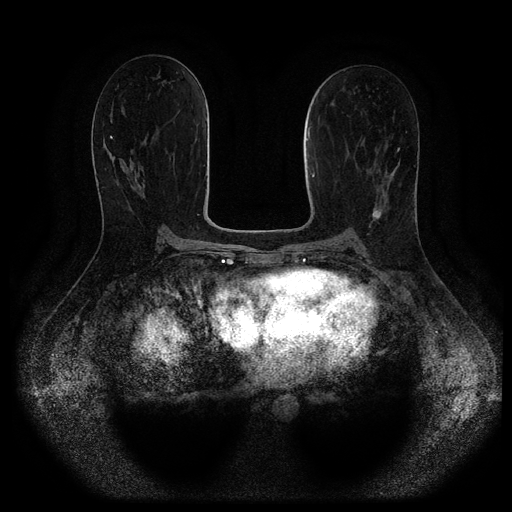
Breast MRI (dynamic contrast-enhanced, multi-phase), one axial slice; slice 55 of 116 in the series (ordered by position); dynamic contrast-enhanced series, time point 2 of 5 at this slice position (early post-contrast); 1.5 T; TE 2.6 ms, TR 5.3 ms; 2 mm slice thickness; 512 × 512 image matrix. Female patient, age 45 years.
Structures marked on this image (semi-automatic segmentation, software-assisted and operator-edited):
- breast lesion (labelled 'tumour' in the annotation; benign lesions carry a separate 'benign' label): bounding box (x1, y1, x2, y2) in pixels: (372, 199, 383, 224)